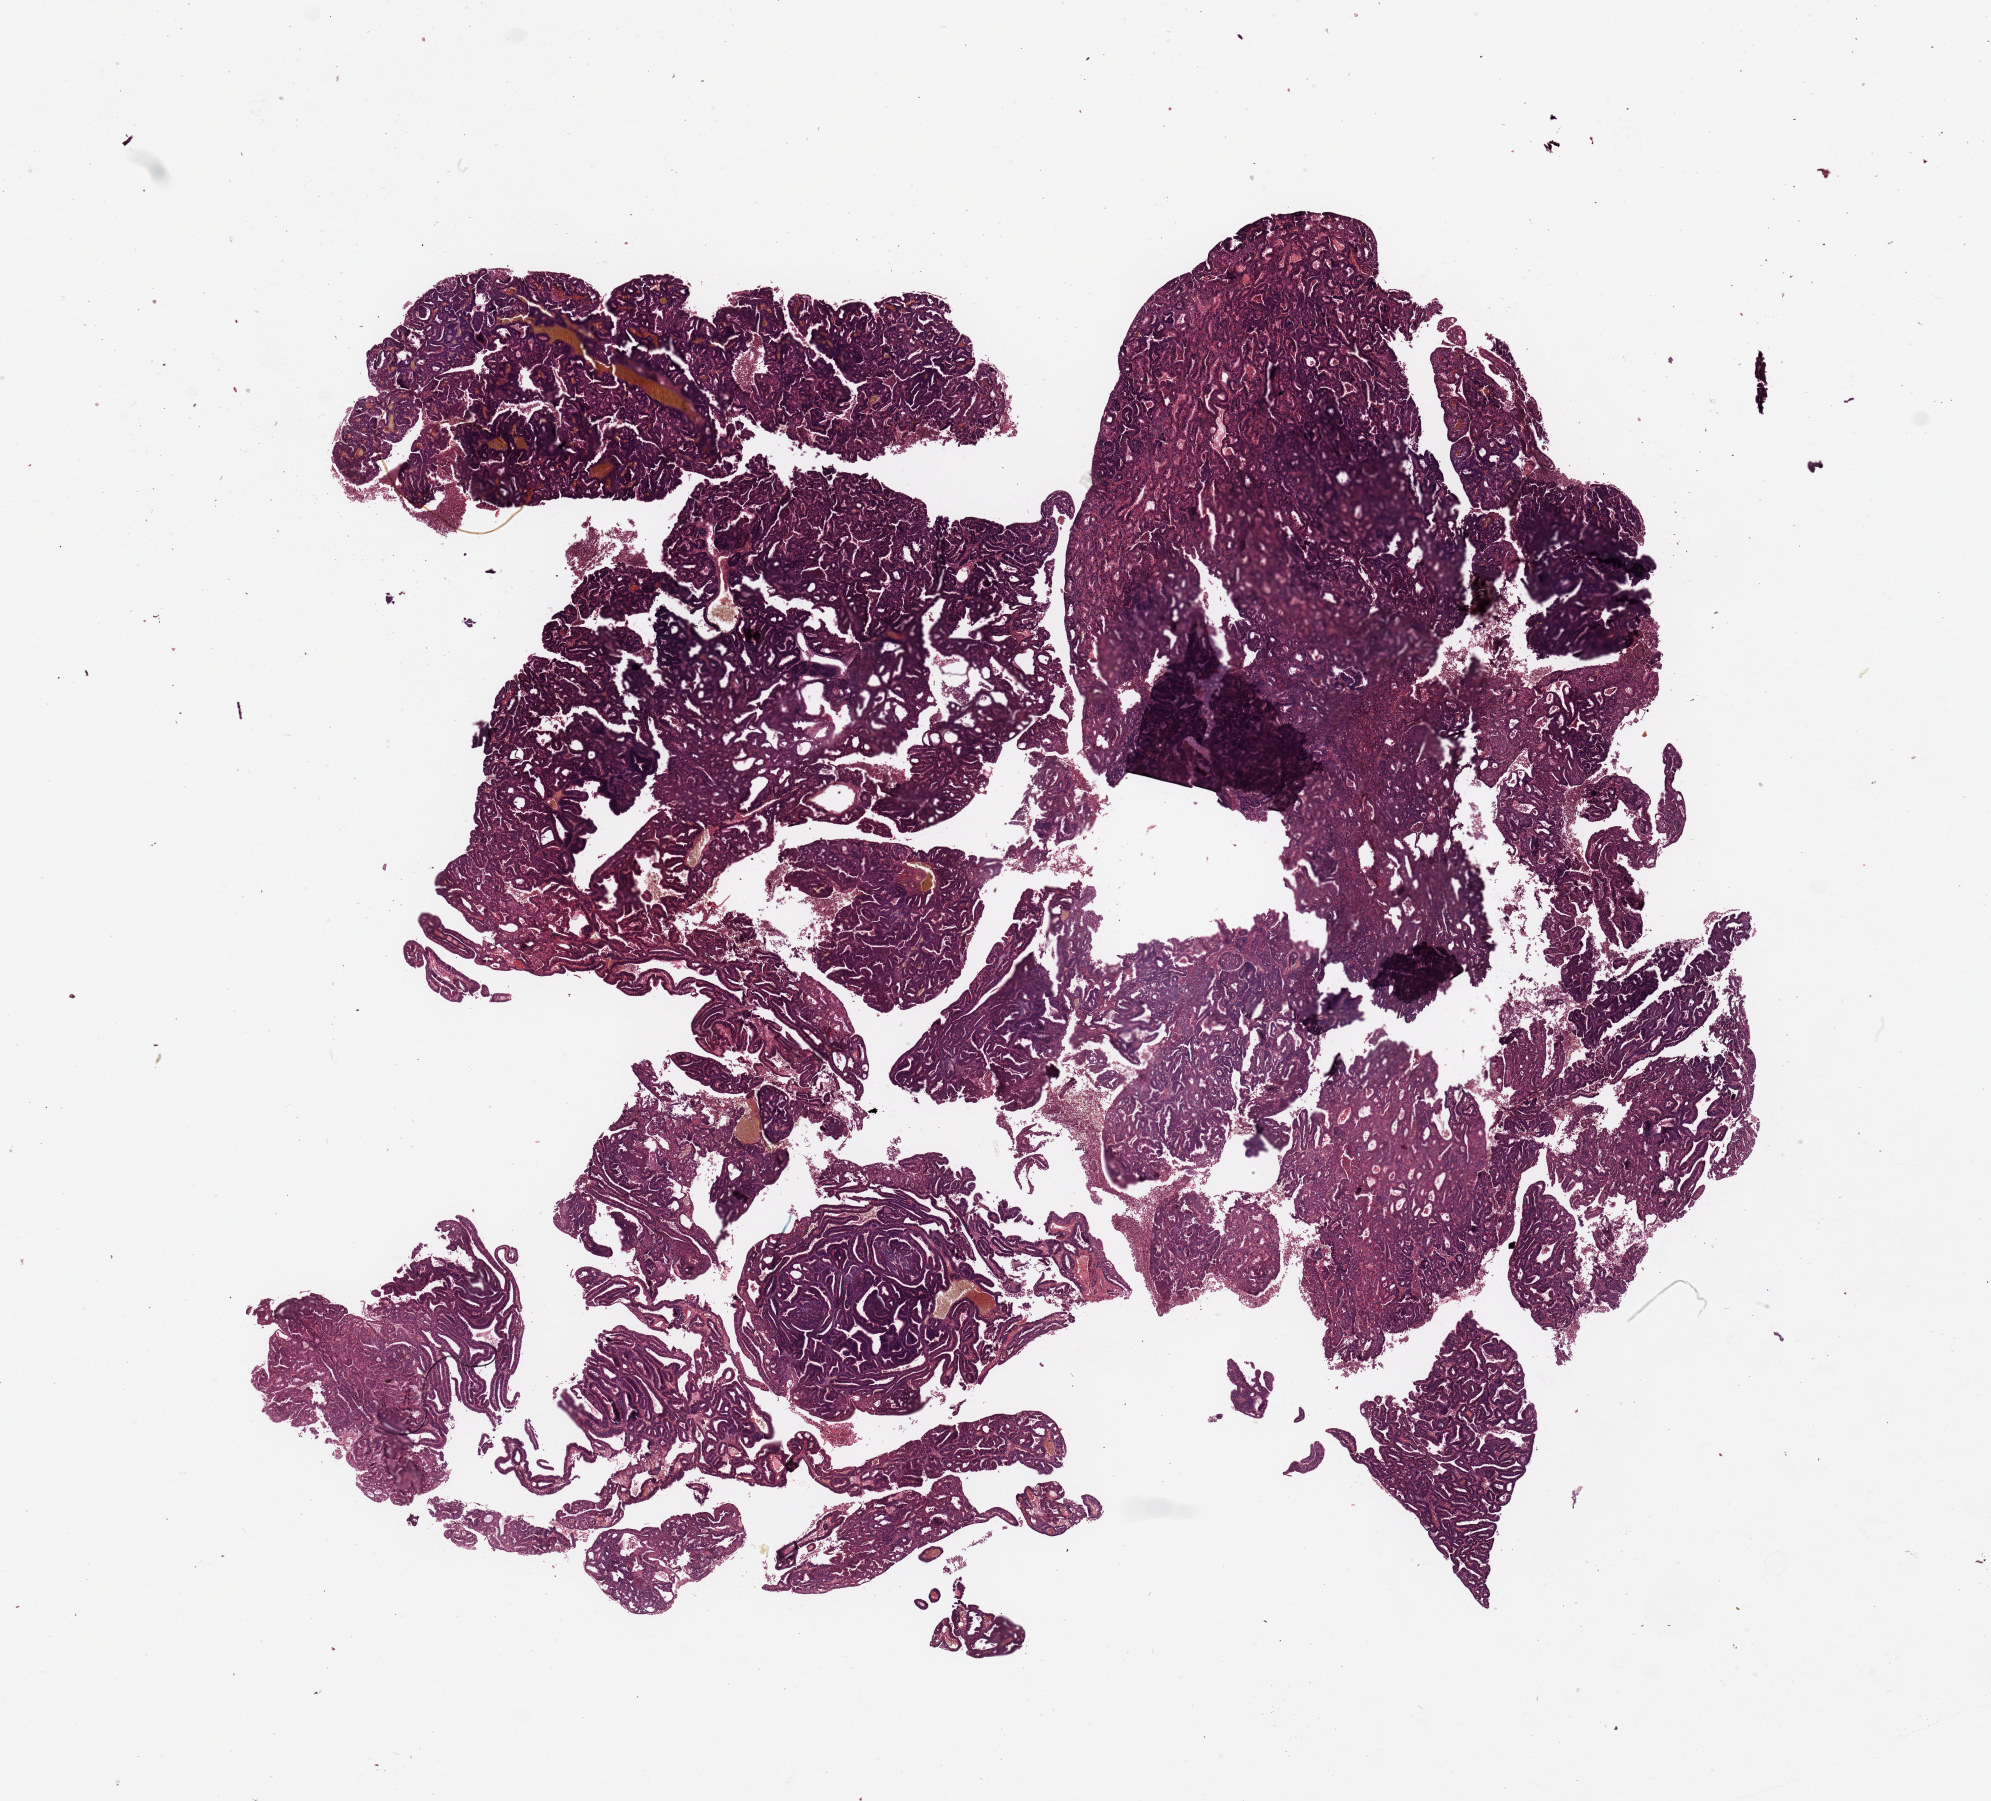
H&E whole-slide image, shown as a low-resolution overview of the whole scanned area (about 15.8 x 14.2 mm, from a 20x scan). Uterus, tissue type not recorded.
Patient diagnosis (cohort enrolment): corpus endometrial carcinoma (uterus).